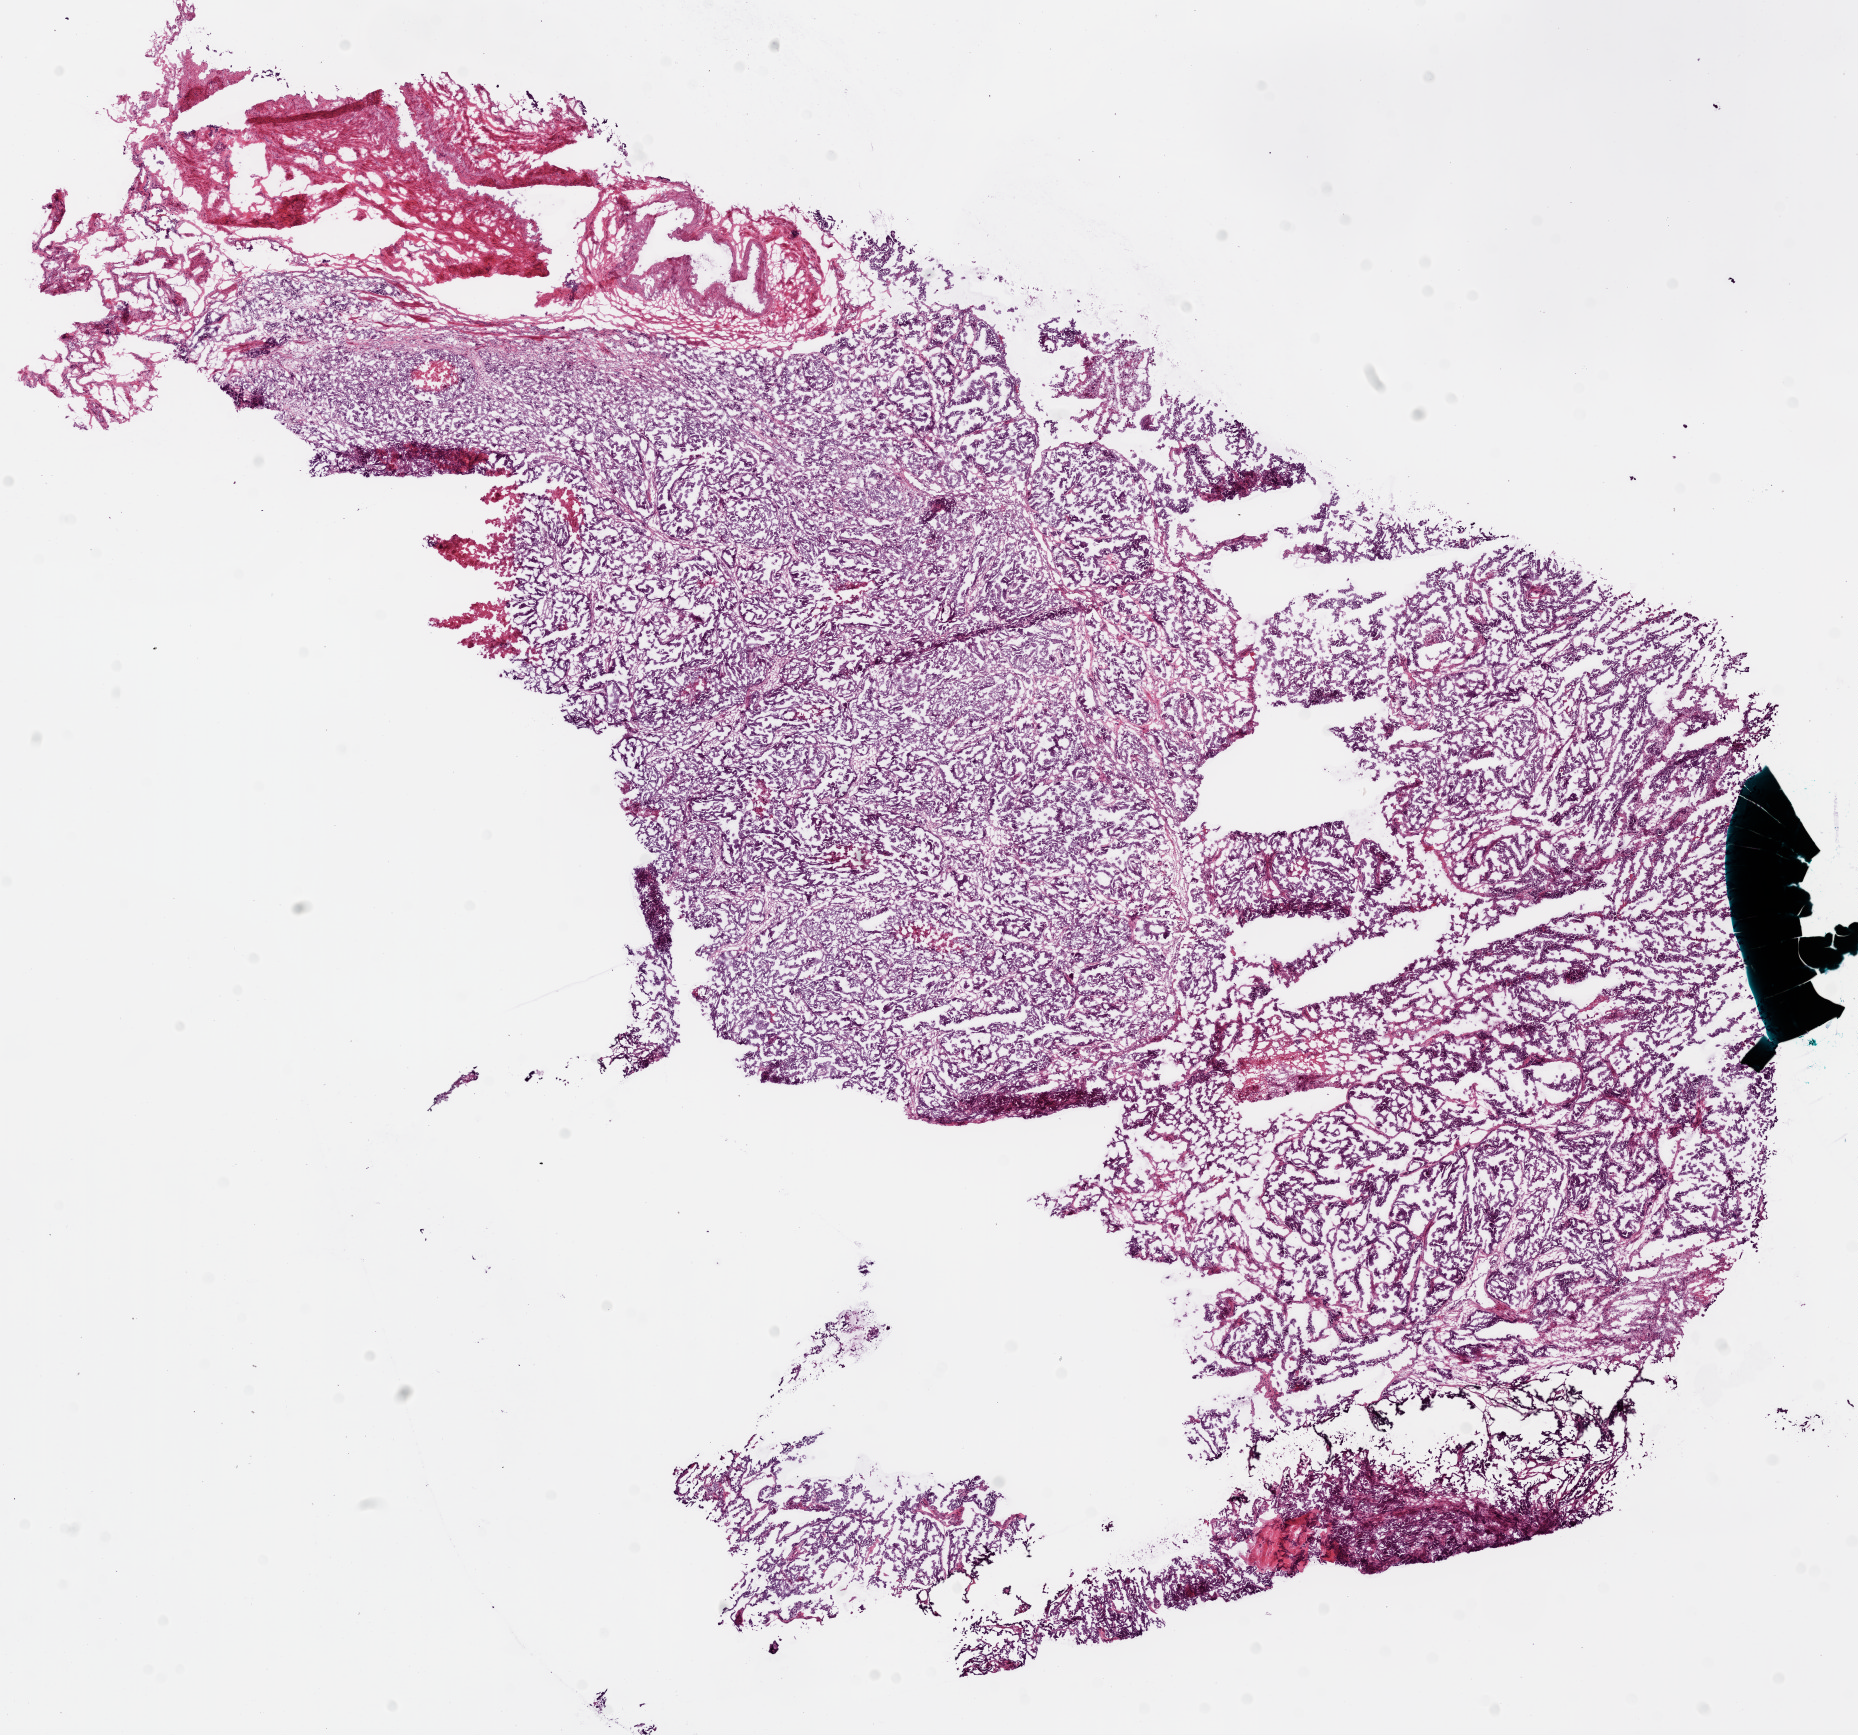
Digitized H&E-stained tissue section (whole slide), whole scanned area (about 15.0 x 14.0 mm, slide scanned at 20x) shown as a low-resolution overview; frozen section from the bottom of the tissue portion; primary tumour sample from the ovary. Female patient; age at initial diagnosis 80 years. Histologic grade: G2 (moderately differentiated). Slide review estimates, as recorded: tumour cells 90%, tumour nuclei 91%, normal cells 0%, stromal cells 9%, necrosis 1%.
Laterality: bilateral. Pathologic diagnosis: Serous cystadenocarcinoma, NOS. FIGO stage: IV.